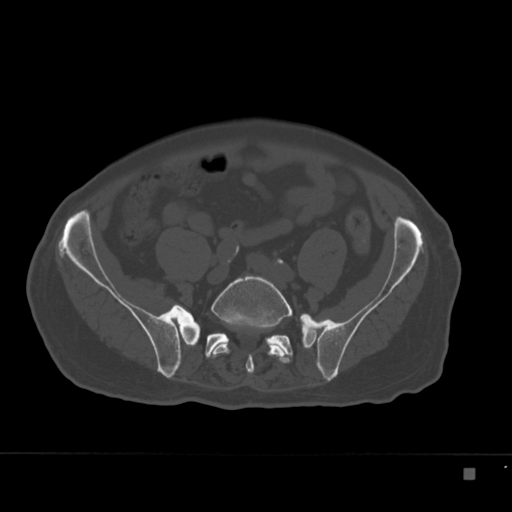
CT including the spine, one axial slice; position 16 of 332 along the scan axis; reconstruction kernel Br40s; bone window (W 1800 / L 400 HU); 1.5 mm slice thickness; 512 × 512 image matrix, field of view 389 × 389 mm. Patient: male, 72 years. Case-level facts recorded for this patient, not image findings: primary cancer: skeletal.
Annotated regions visible in this slice (semi-automatic segmentation, software-assisted and operator-edited):
- L5 vertebra: bounding box <206,276,292,374> (left, top, right, bottom; pixels)